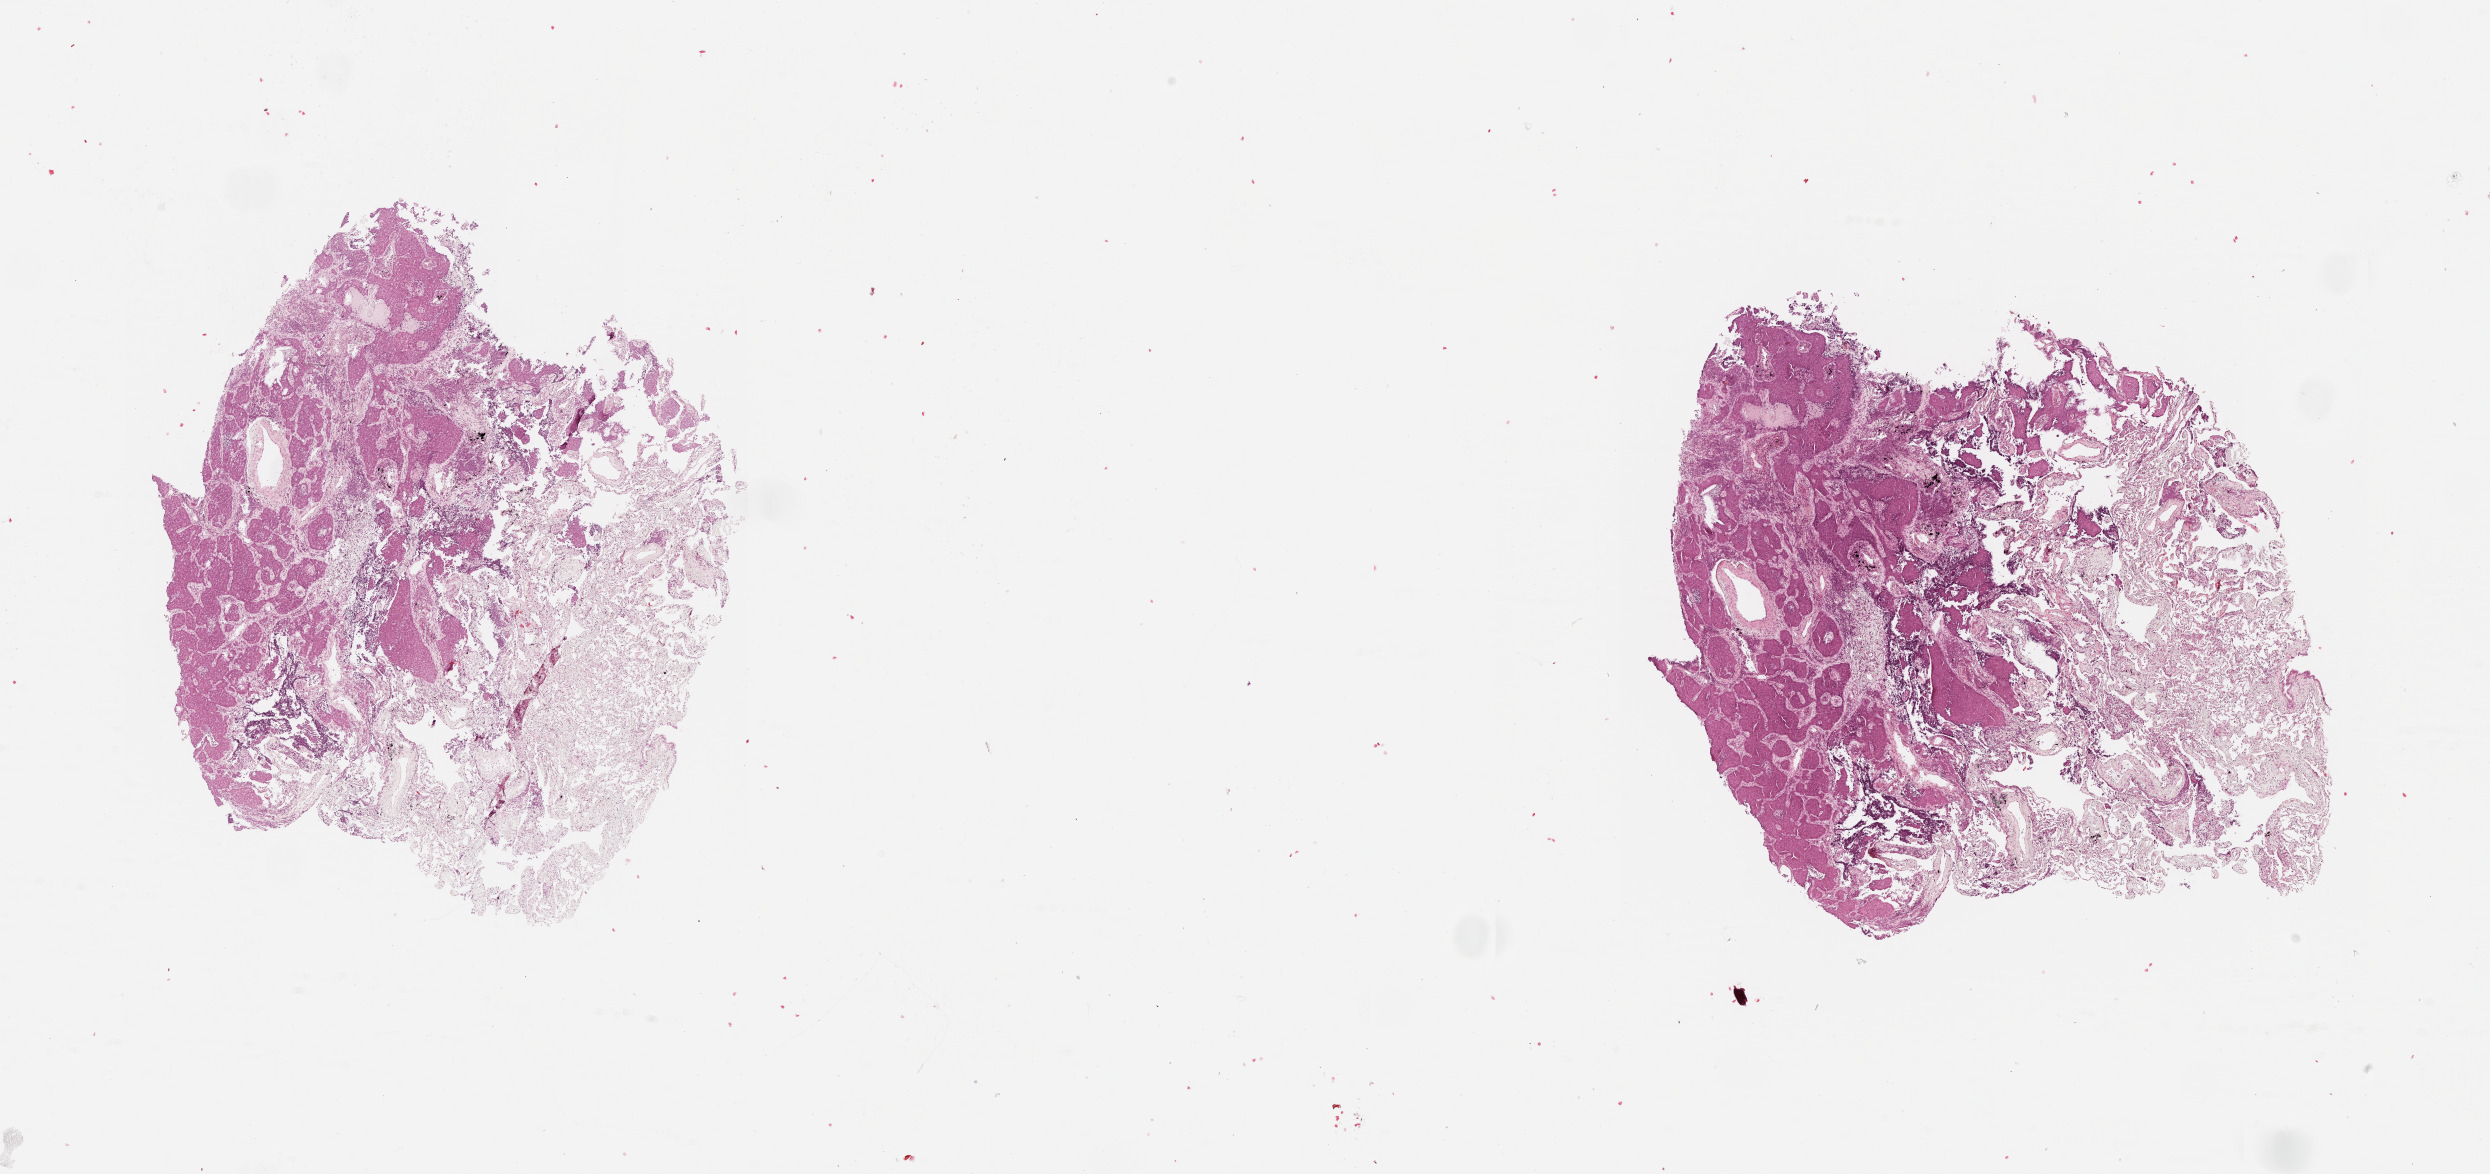
Whole-slide histology image, H&E — a low-resolution overview of the entire scanned area, about 20.0 x 9.5 mm (from a 20x scan), lung, tissue type not recorded.
Patient diagnosis (cohort enrolment): squamous cell carcinoma (lung).